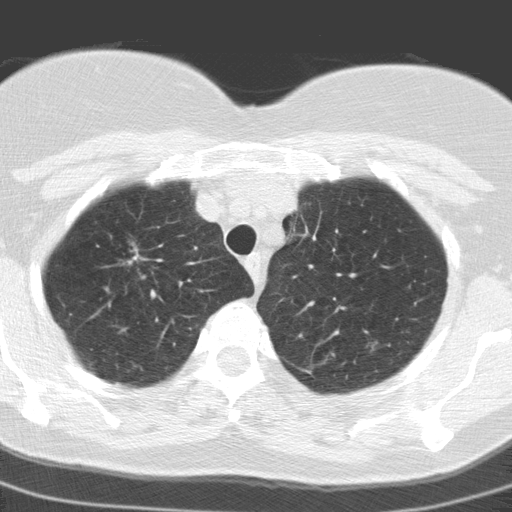
Low-dose screening chest CT, axial slice. Baseline screening round. Lung window (W 1500 / L -600 HU). 3.2 mm slice thickness. Standard (soft-tissue) reconstruction kernel (C). 512 × 512 image matrix. Female, age 60 years at enrolment. Former smoker at enrolment.
• Expert-annotated lung lesion, bounding box (x1, y1, x2, y2) in pixels: (100, 235, 161, 282).
• No non-calcified nodule or mass ≥4 mm was recorded by the screening reader at this exam.
• Official screen result: negative screen, minor abnormalities not suspicious for lung cancer.